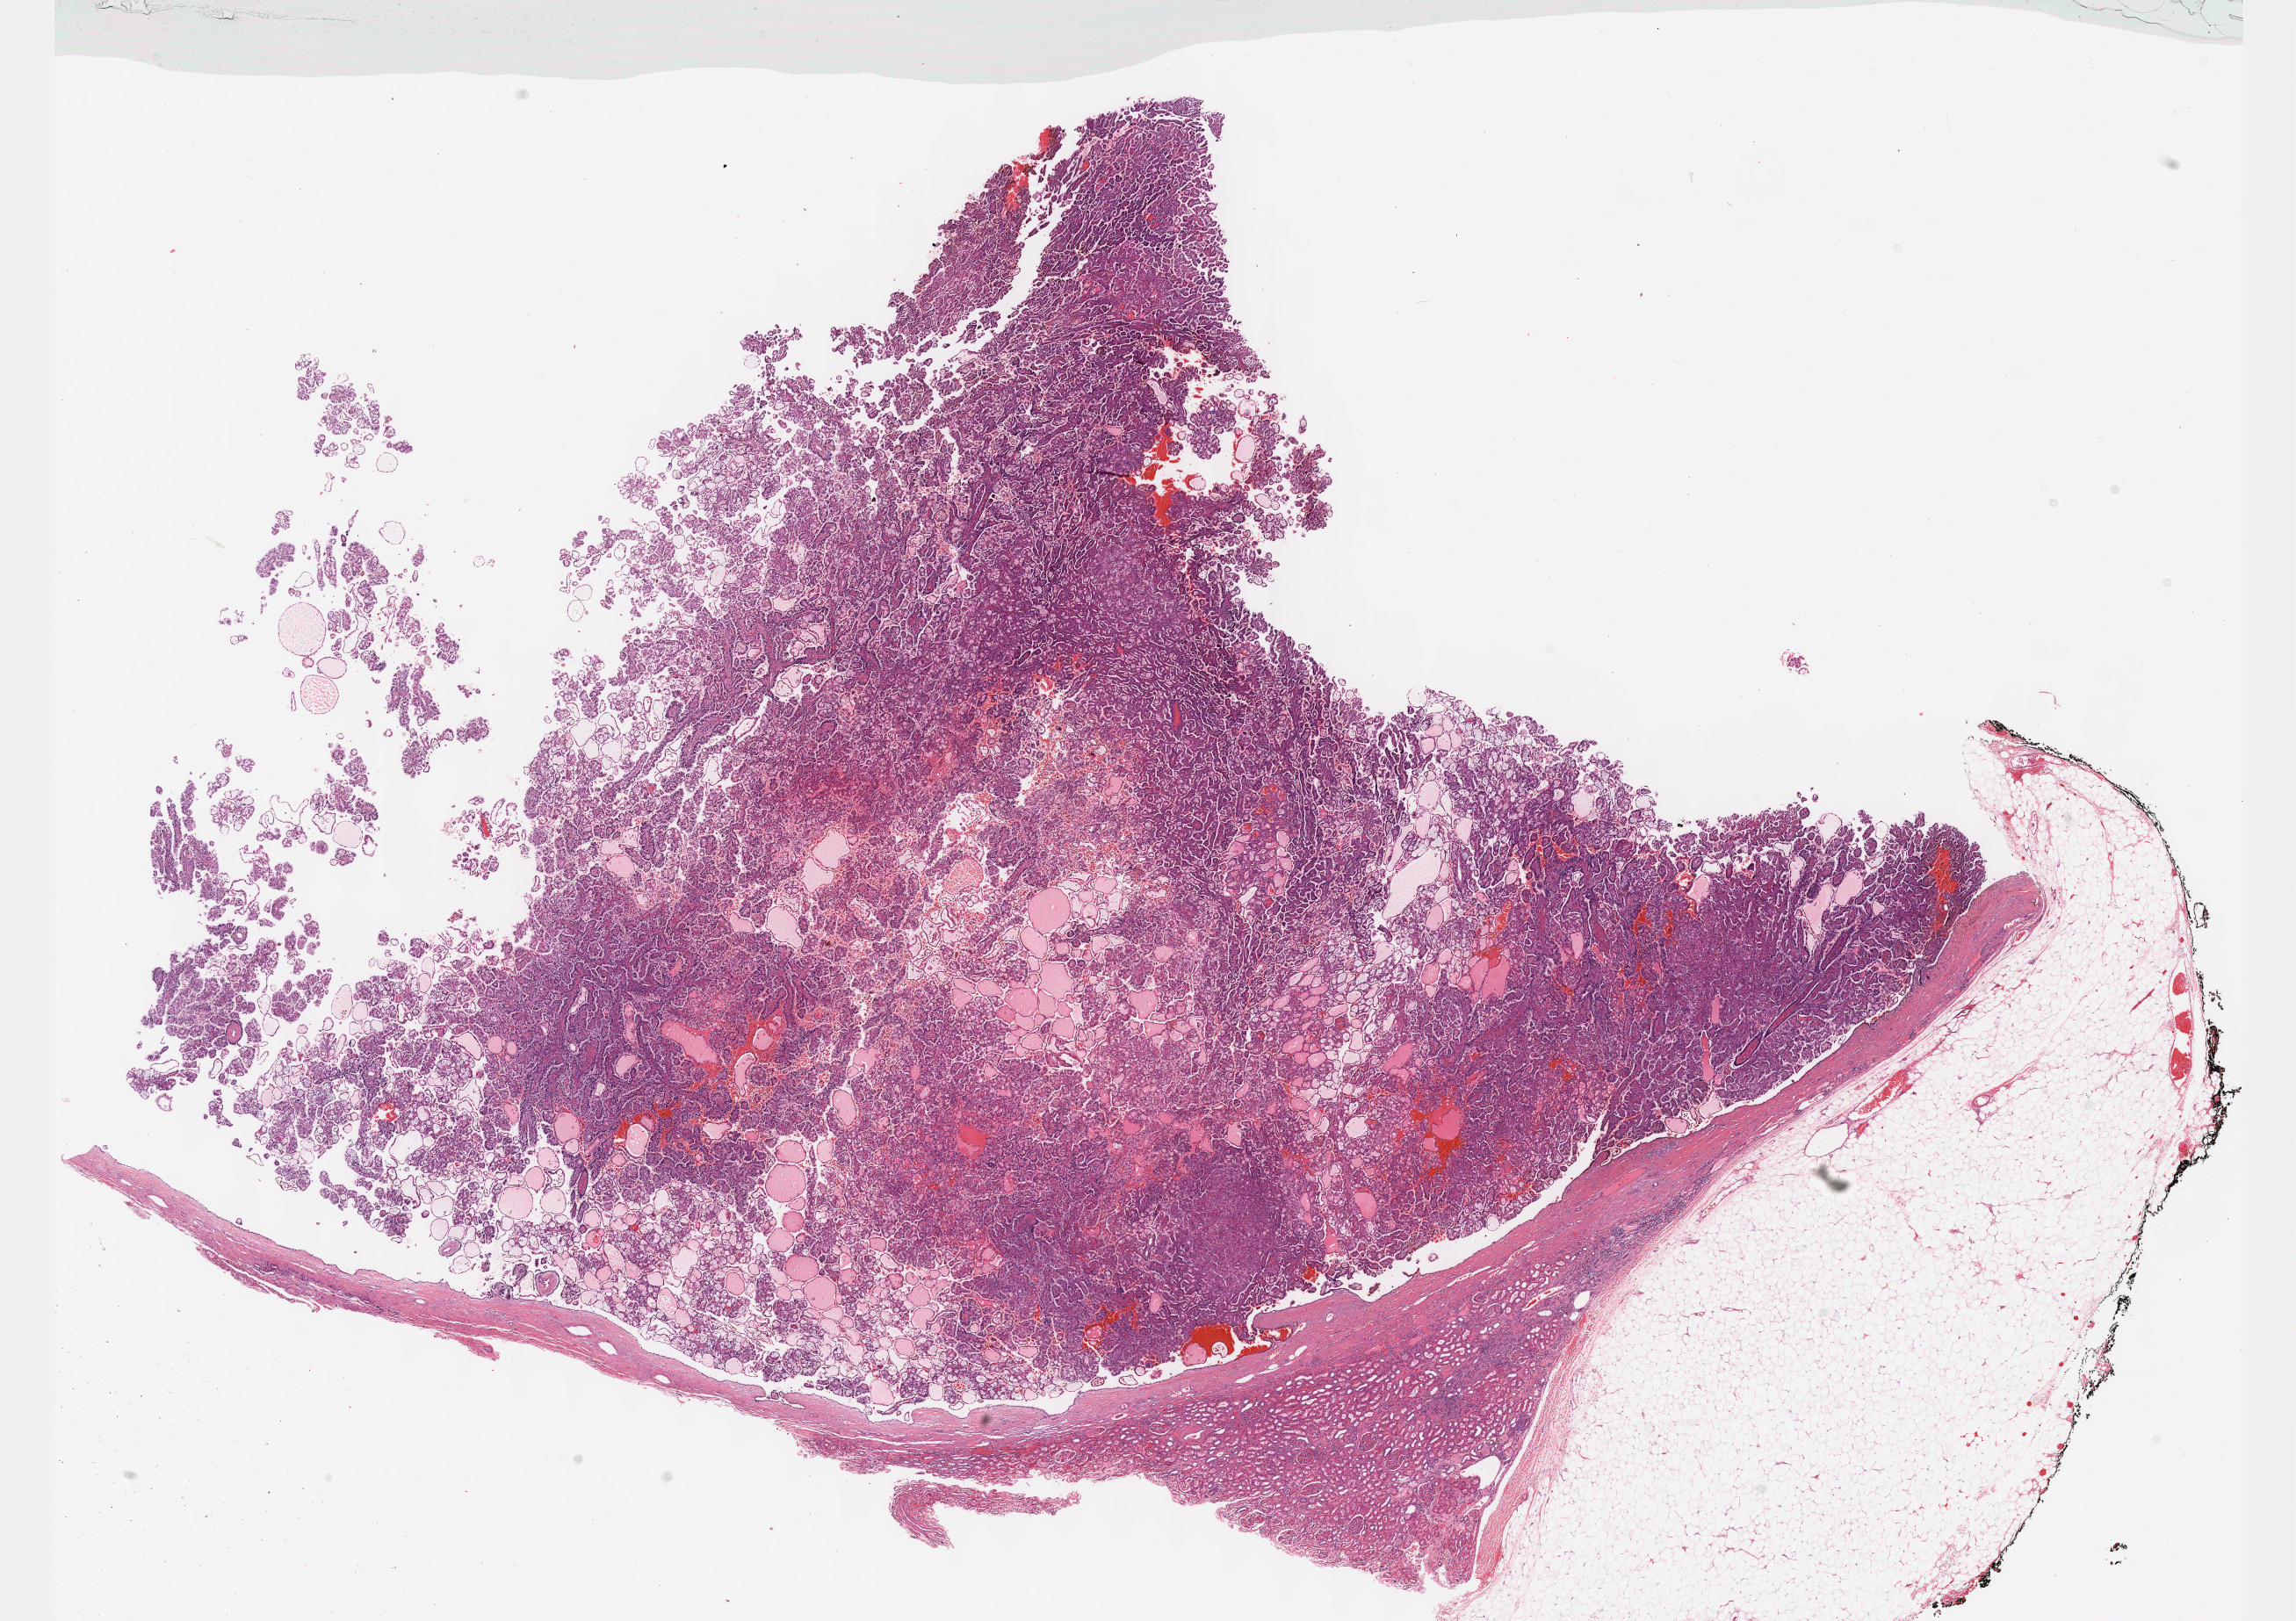
Whole-slide histology image, H&E — whole scanned area (about 21.1 x 14.9 mm, slide scanned at 40x) shown as a low-resolution overview, formalin-fixed paraffin-embedded (FFPE) diagnostic section, kidney, primary tumour sample. Patient: male, age at initial diagnosis 60 years.
AJCC pathologic stage: I (6th edition). Pathologic diagnosis: Papillary adenocarcinoma, NOS. TNM: T1a NX MX. Laterality: right.